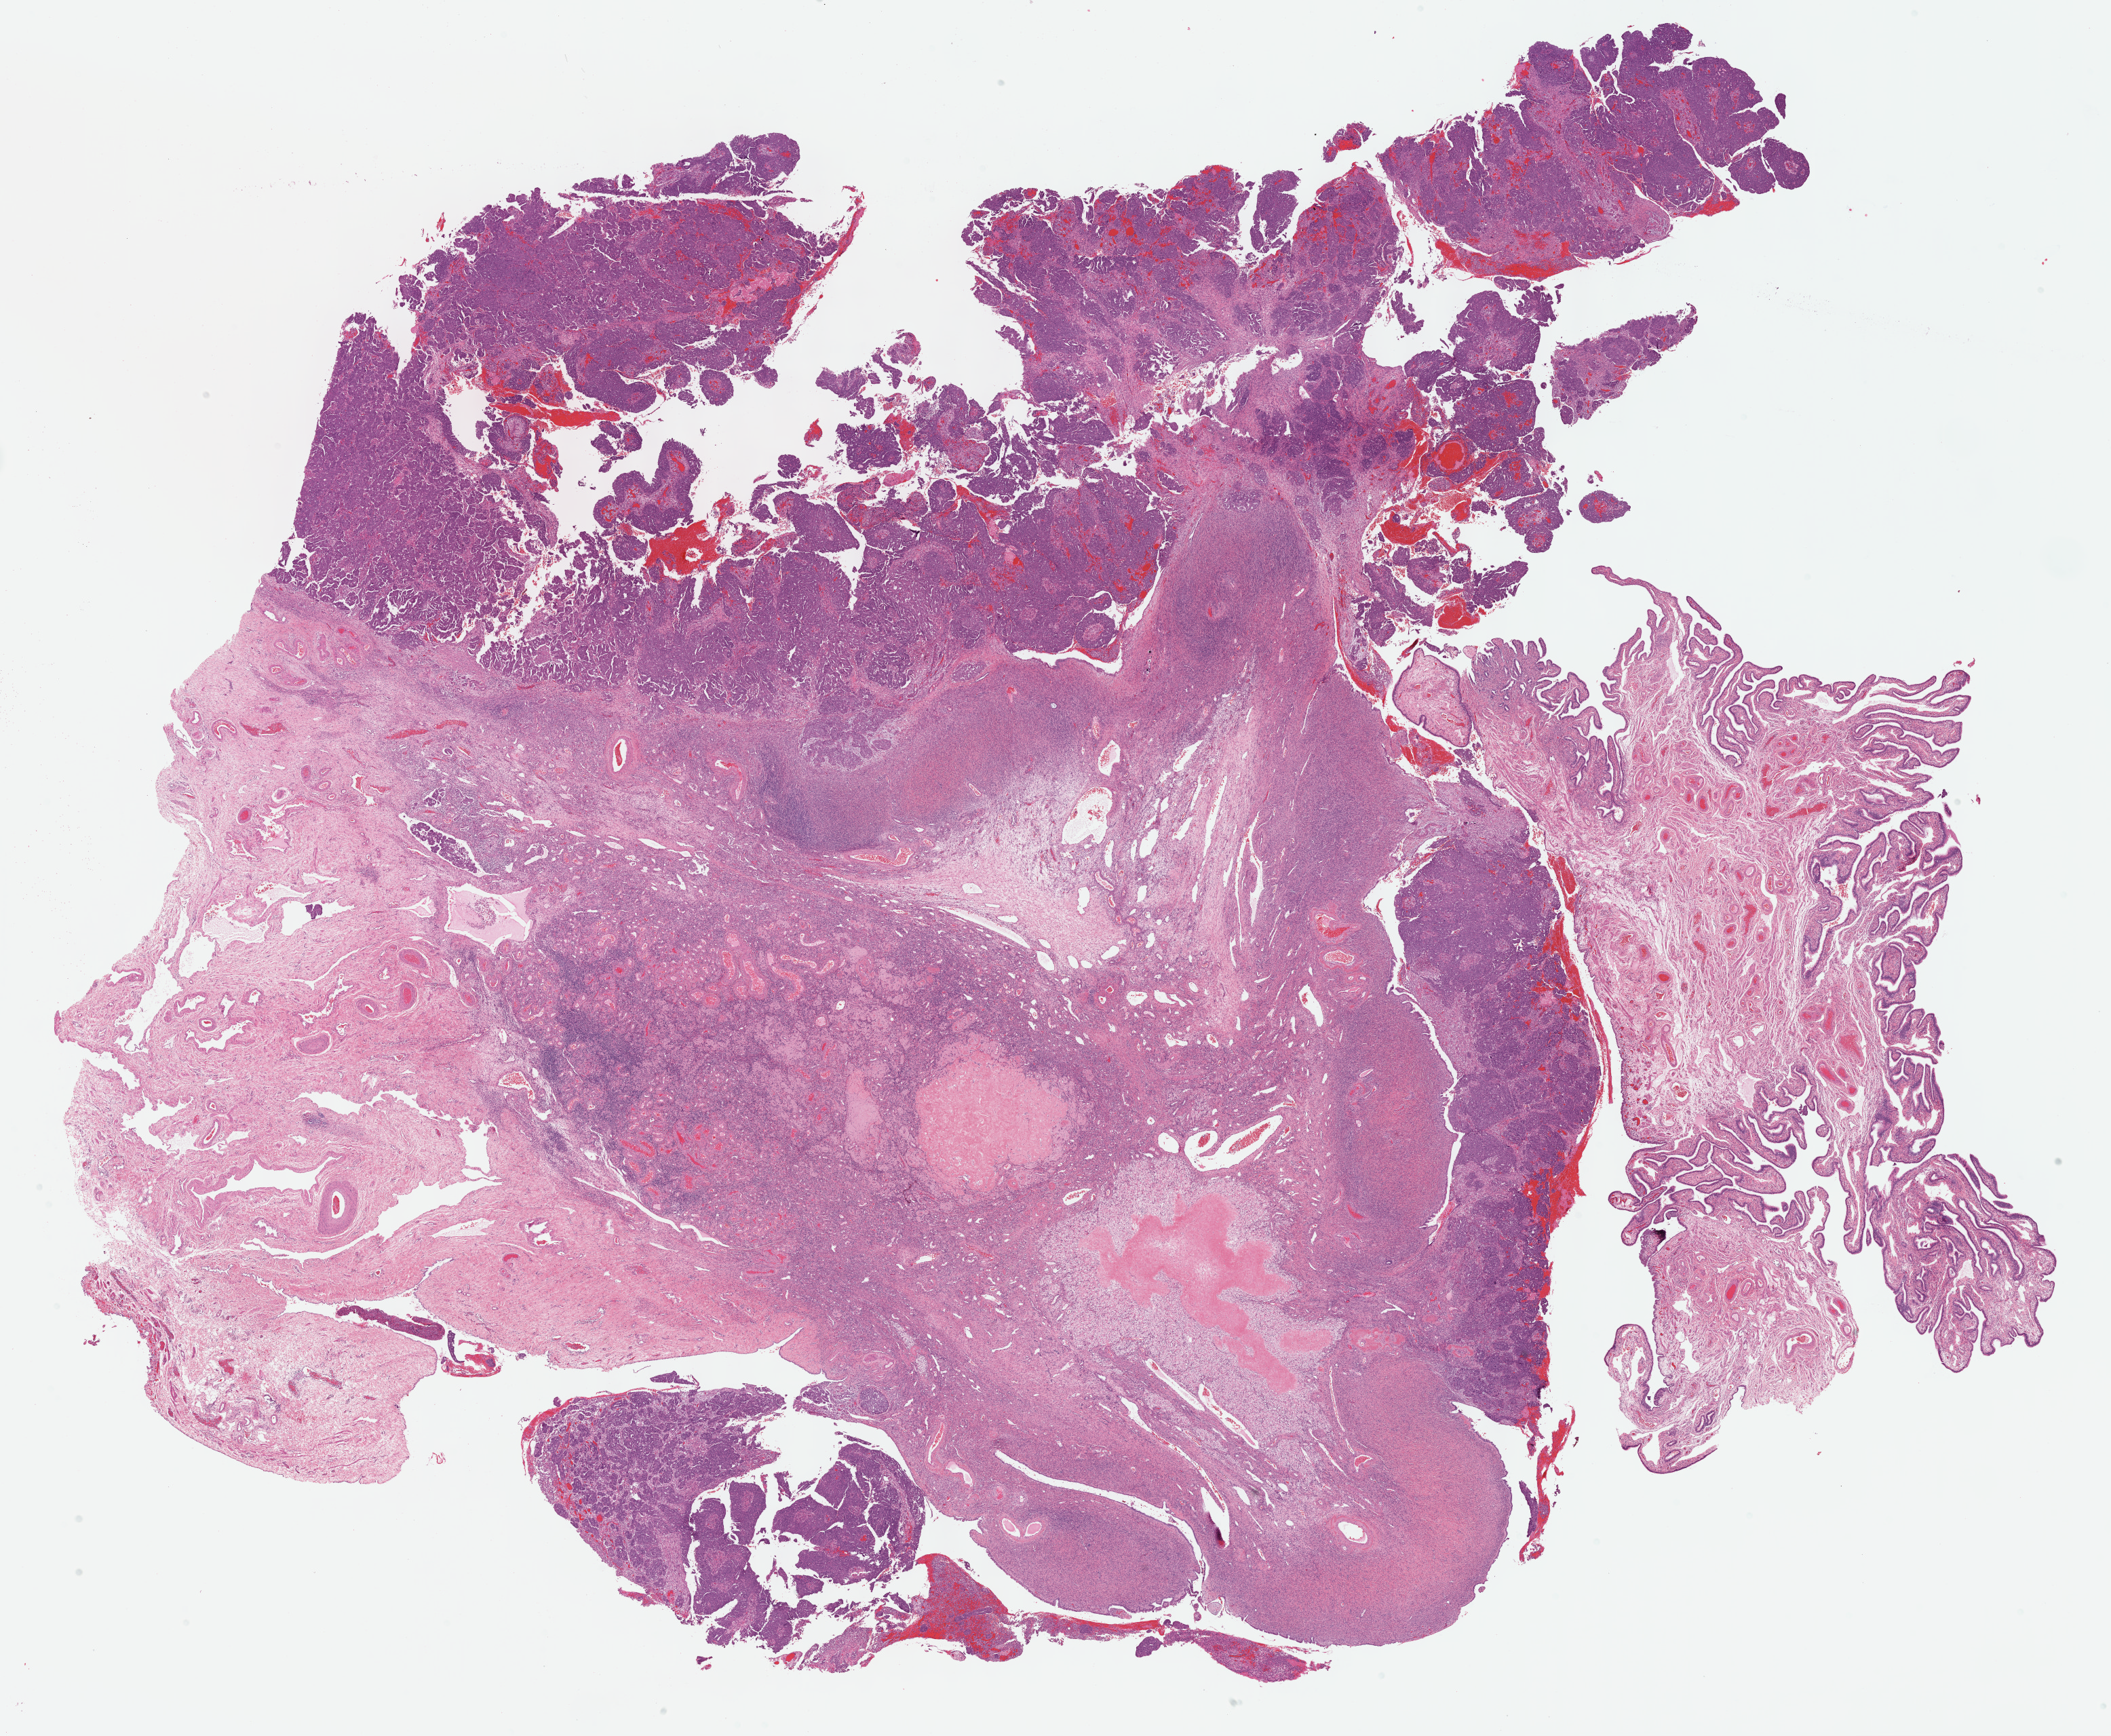
Whole-slide histology image, Hematoxylin and eosin (H&E) stained — shown as a low-resolution overview of the whole scanned area (about 25.2 x 20.7 mm), formalin-fixed paraffin-embedded (FFPE) diagnostic section, ovary, primary tumour sample. Patient: female, age at initial diagnosis 48 years. Histologic grade: G3 (poorly differentiated).
Diagnosis: Serous cystadenocarcinoma, NOS. Laterality: right. FIGO stage: IIIC.